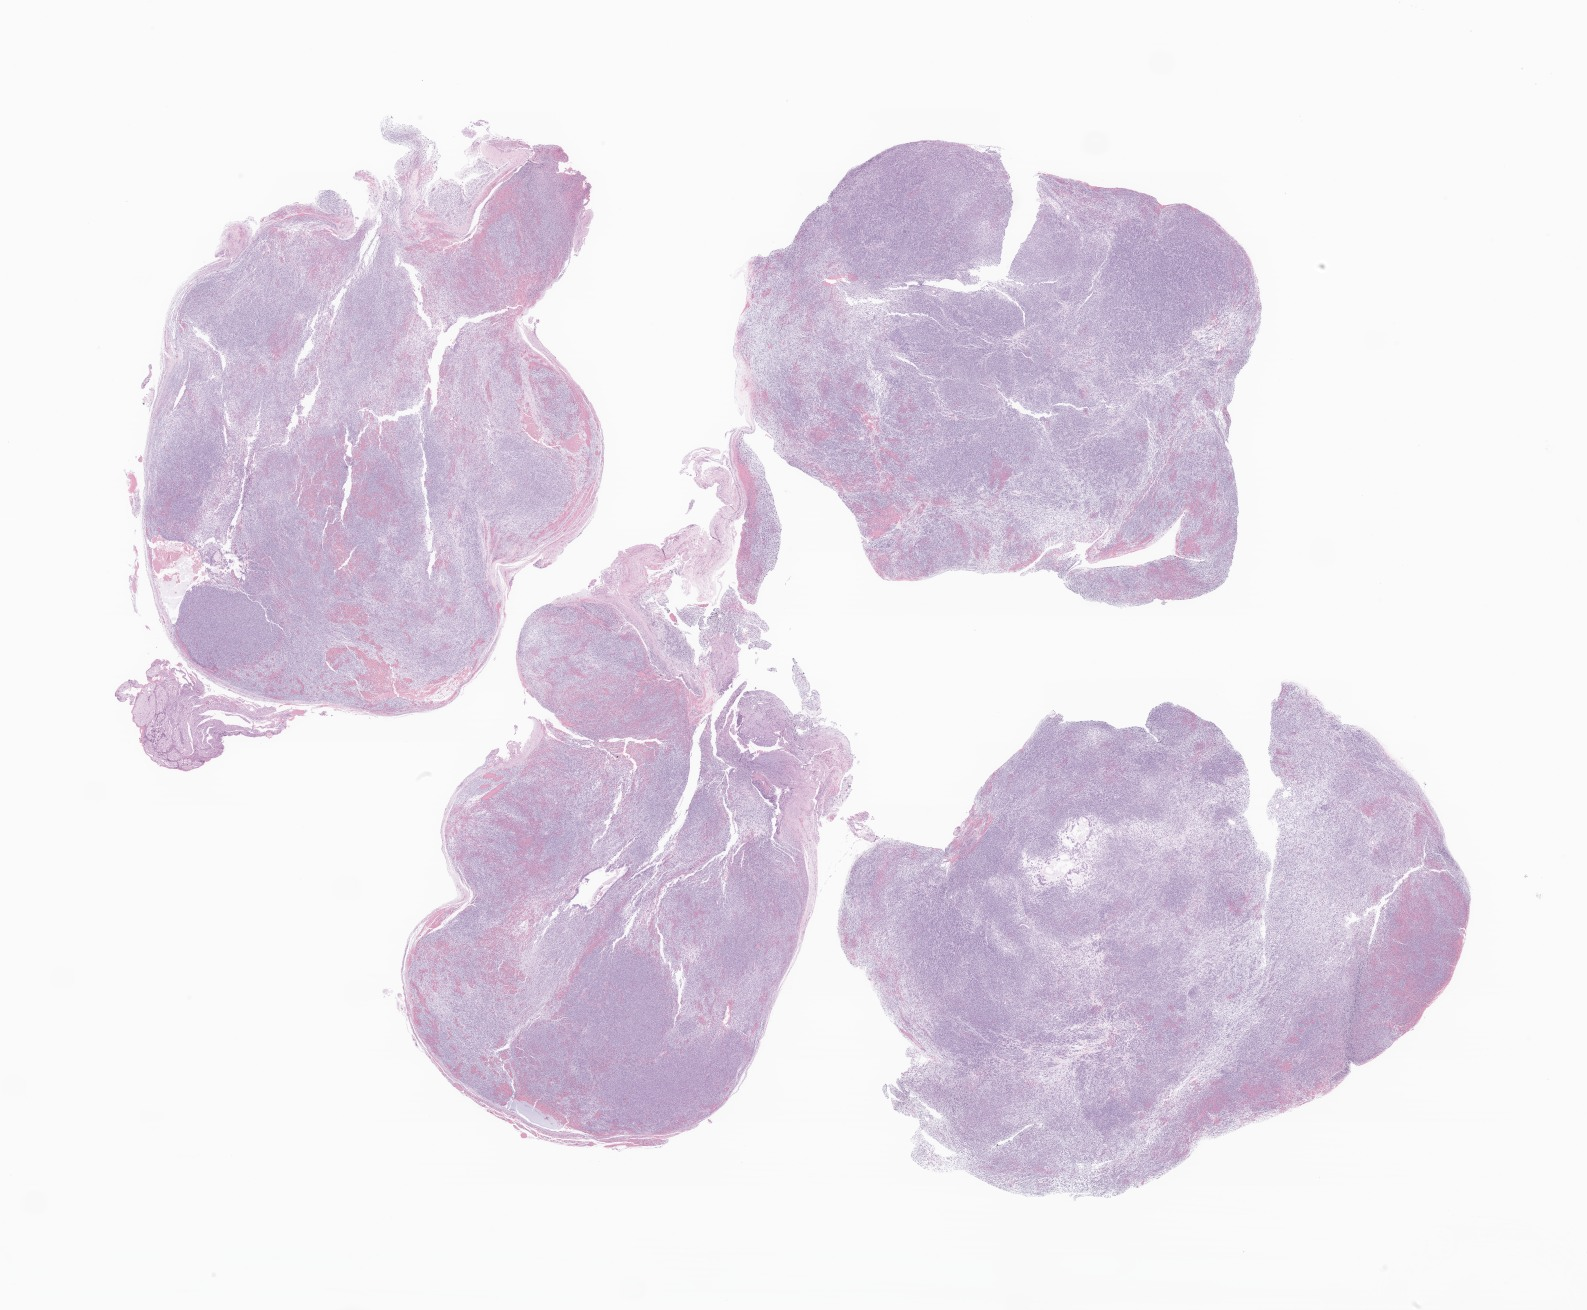
Digitized haematoxylin and eosin-stained section of tumor tissue from the vertebral column — a low-resolution overview of the entire scanned area, about 26.8 x 22.1 mm, formalin-fixed paraffin-embedded section. Patient female; age 82 months (6 years 10 months).
Diagnosis: Rhabdoid tumor, NOS.